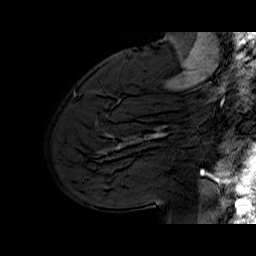
Breast MRI (dynamic contrast-enhanced), one sagittal slice. Position 47 of 70 along the scan axis. Dynamic contrast-enhanced series, time point 2 of 6 at this slice position (early post-contrast). 1.5 T. TE 6.5 ms, TR 33 ms. 256 × 256 image matrix, field of view 200 × 200 mm. Female patient. Case-level facts recorded for this patient, not image findings: setting: breast cancer imaged before/during neoadjuvant chemotherapy; receptor status: HER2-positive.
Outlined on this slice (semi-automatically segmented with operator editing):
- analysis volume of interest (the breast-tissue region the enhancement analysis was run in; not a lesion): bounding box <113,112,174,170> (left, top, right, bottom; pixels)
- tumour enhancement mask (voxels above the 100 % enhancement threshold inside the analysis volume of interest): <117,133,163,148>